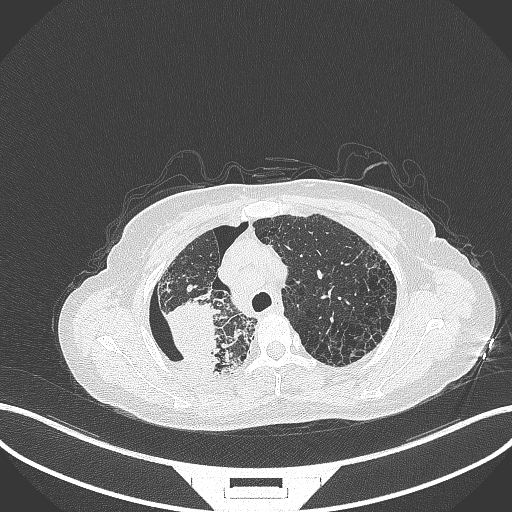
Chest CT, one axial slice. Slice 273 of 408 in the series (ordered by position). 120 kVp. Lung window (W 1500 / L -600 HU). 1 mm slice thickness. 512 × 512 image matrix, field of view 400 × 400 mm. Female patient, age 64 years. Case-level facts recorded for this patient, not image findings: clinical TNM (as recorded): T3 N3 M0.
Outlined on this slice (bounding box drawn by a radiologist):
- lung tumour (recorded histology: squamous cell carcinoma): bounding box (x1, y1, x2, y2) in pixels: (161, 296, 225, 376)